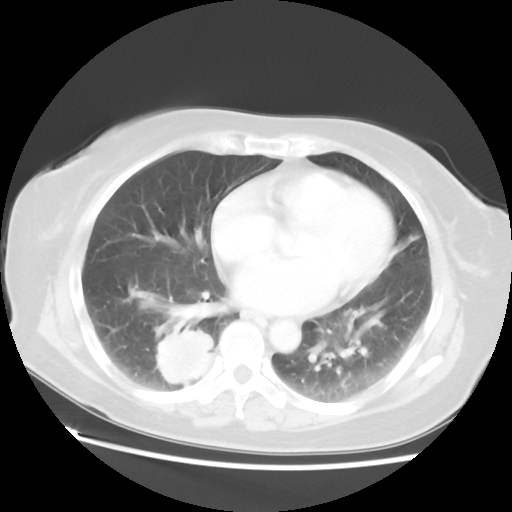
Chest CT, one axial slice. Slice 24 of 52 in the series (ordered by position). 120 kVp. Lung window (W 1500 / L -600 HU). 5 mm slice thickness. 512 × 512 image matrix, field of view 356 × 356 mm. Patient: female, 69 years. Case-level facts recorded for this patient, not image findings: clinical TNM (as recorded): T2 N1 M1a.
Structures marked on this image (rectangle marked by the reading radiologist):
- lung tumour (recorded histology: adenocarcinoma): bounding box [x1, y1, x2, y2] px = [152, 324, 216, 386]